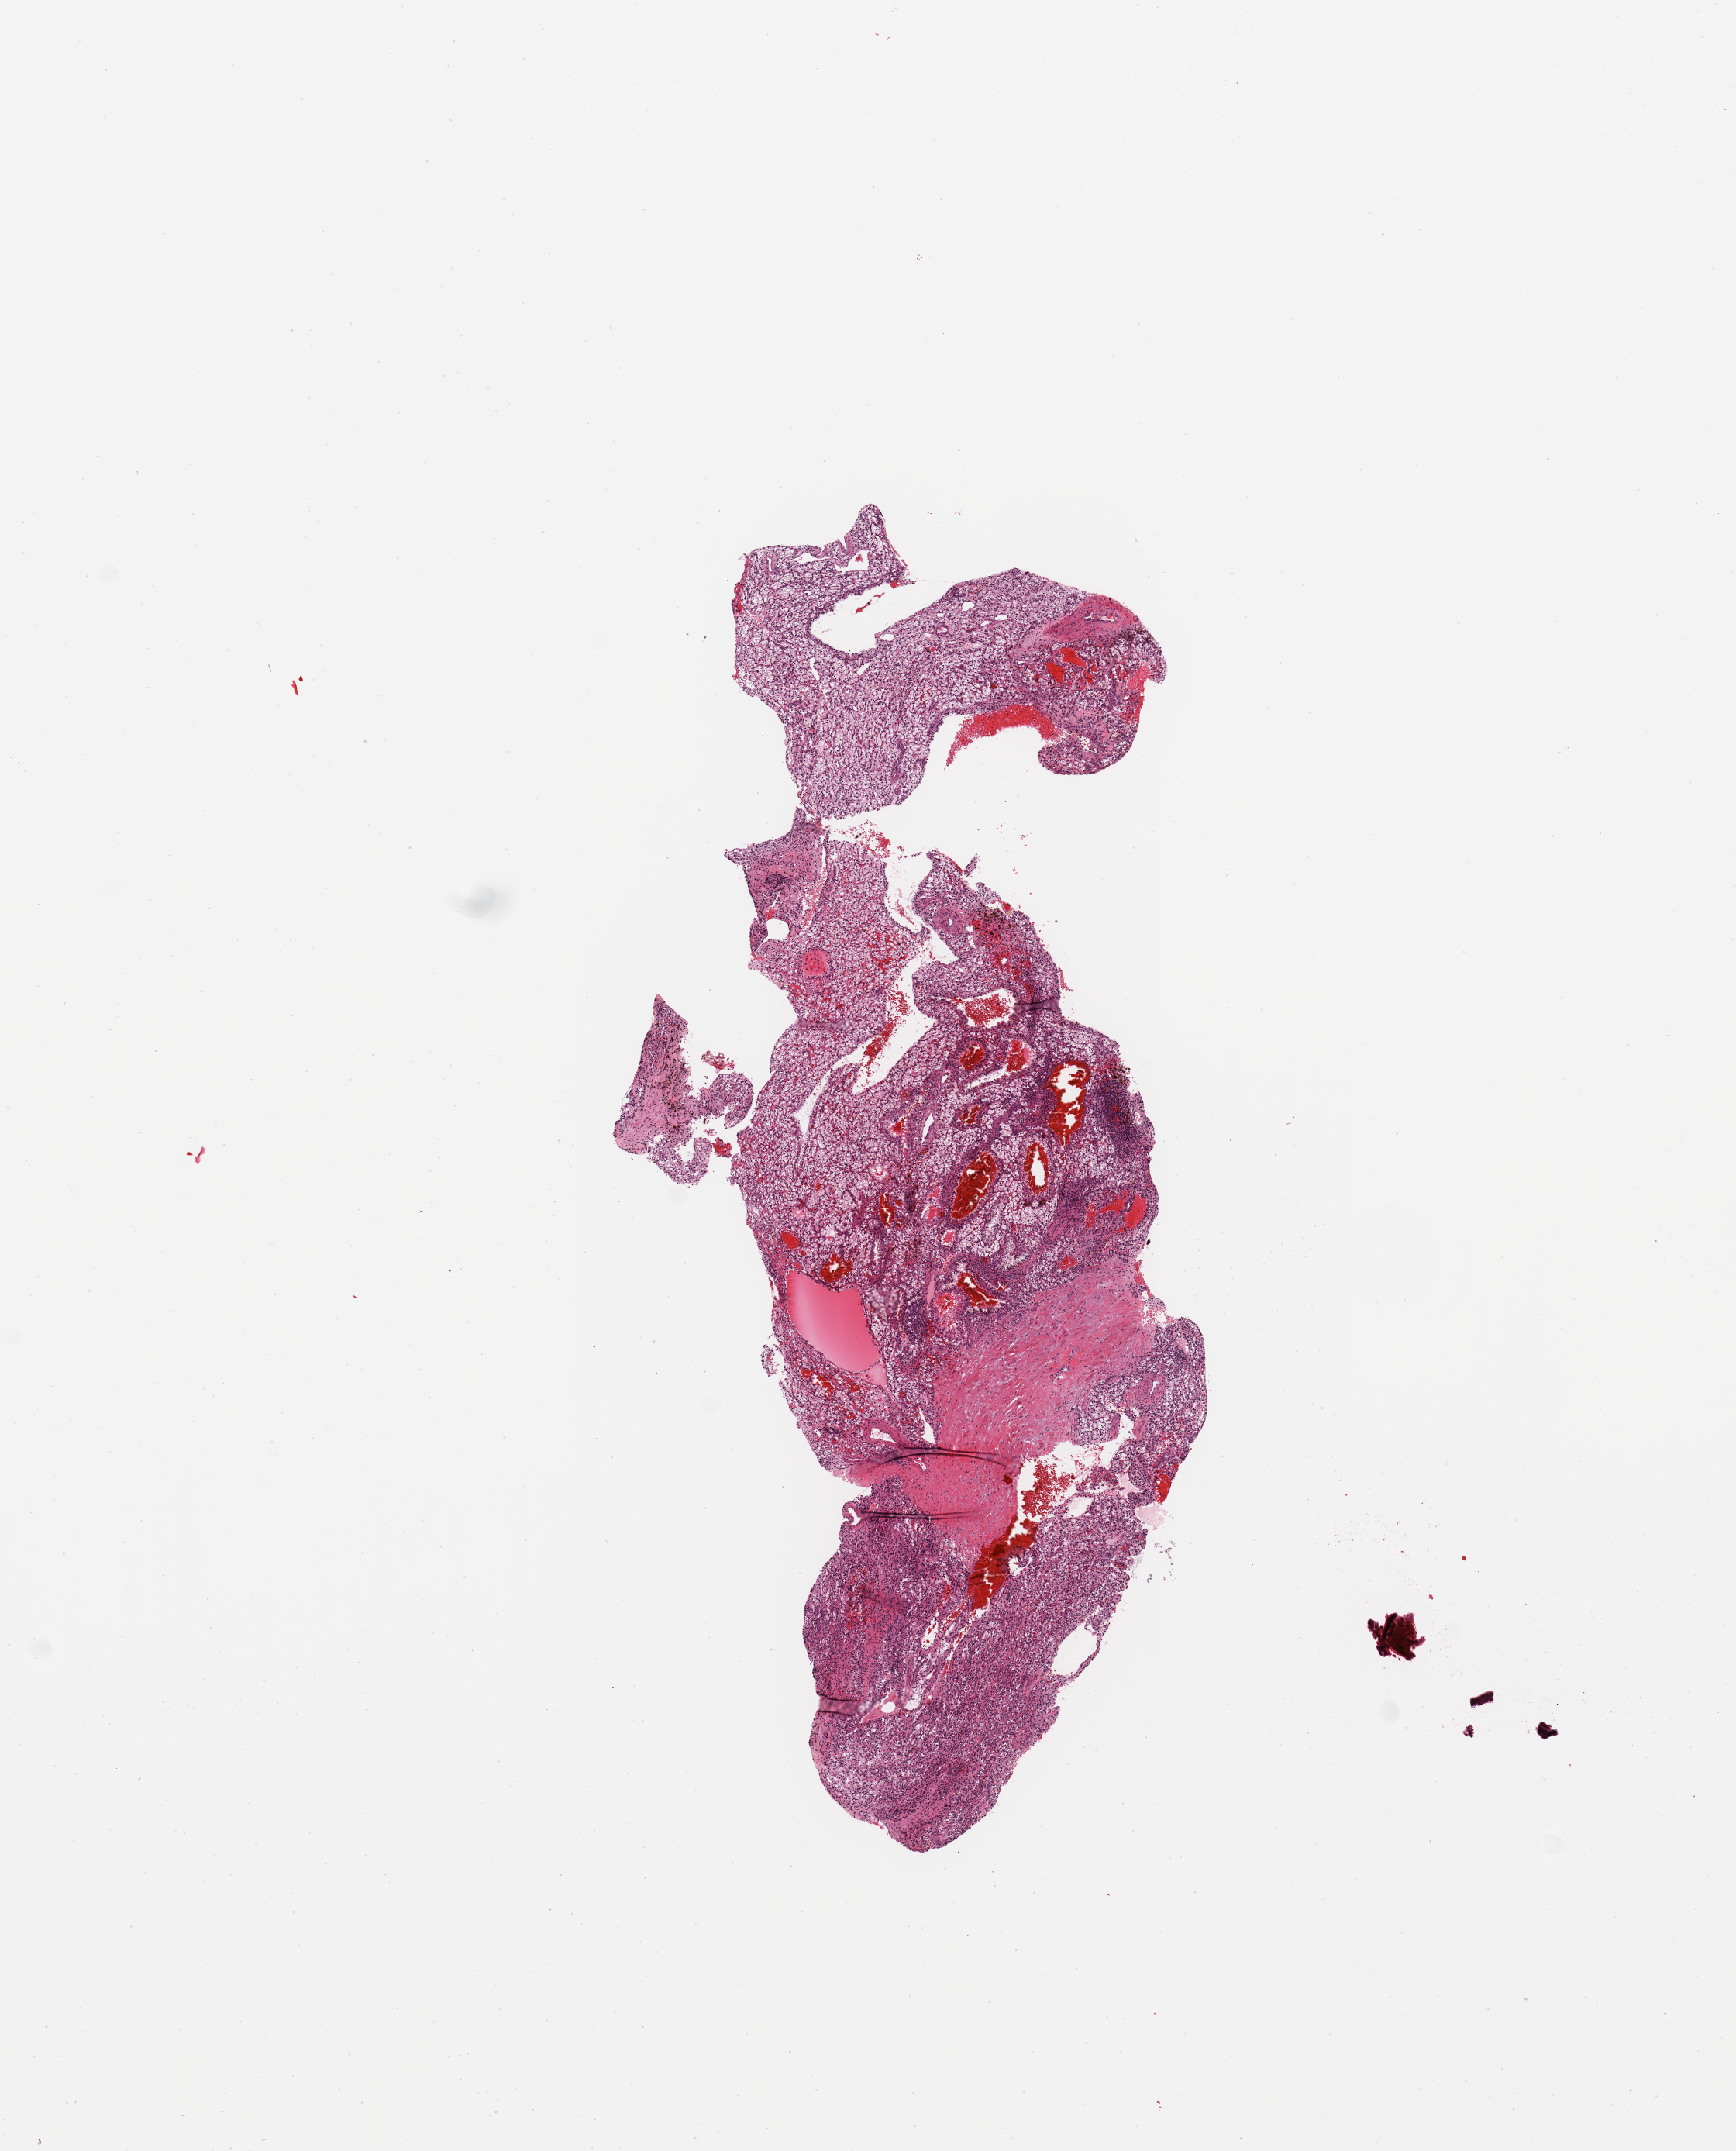
Whole-slide histology image, H&E — low-resolution overview of the scanned area, about 8.9 x 11.0 mm. Tumour tissue sample, sampled site: kidney. Patient: male, age 67 years. Histologic grade: G2 (moderately differentiated). Composition of this section per pathologist review: tumour nuclei 90%, necrosis 2%.
Primary tumour site (as recorded): lower pole. Diagnosis: Renal cell carcinoma, NOS. AJCC pathologic stage: I.